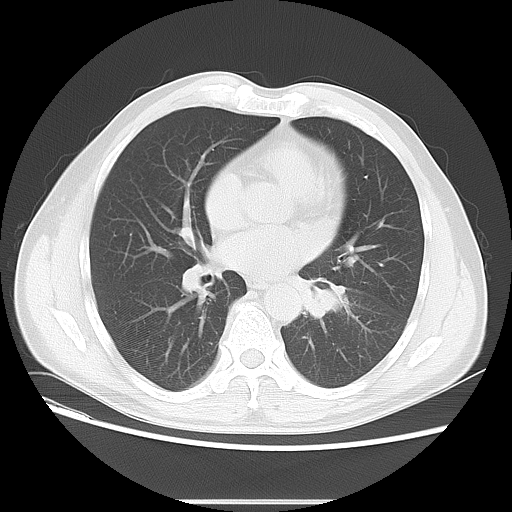
Chest CT, one axial slice; slice 27 of 59 in the series (ordered by position); reconstruction kernel LUNG; 120 kVp; lung window (W 1500 / L -600 HU); 5 mm slice thickness; 512 × 512 image matrix, field of view 378 × 378 mm. Male patient, age 59 years. From the clinical record (not read from this slice): clinical TNM (as recorded): T2 N3 M0.
Structures marked on this image (bounding box drawn by a radiologist):
- lung tumour (recorded histology: small cell carcinoma): bounding box <298,275,346,326> (left, top, right, bottom; pixels)